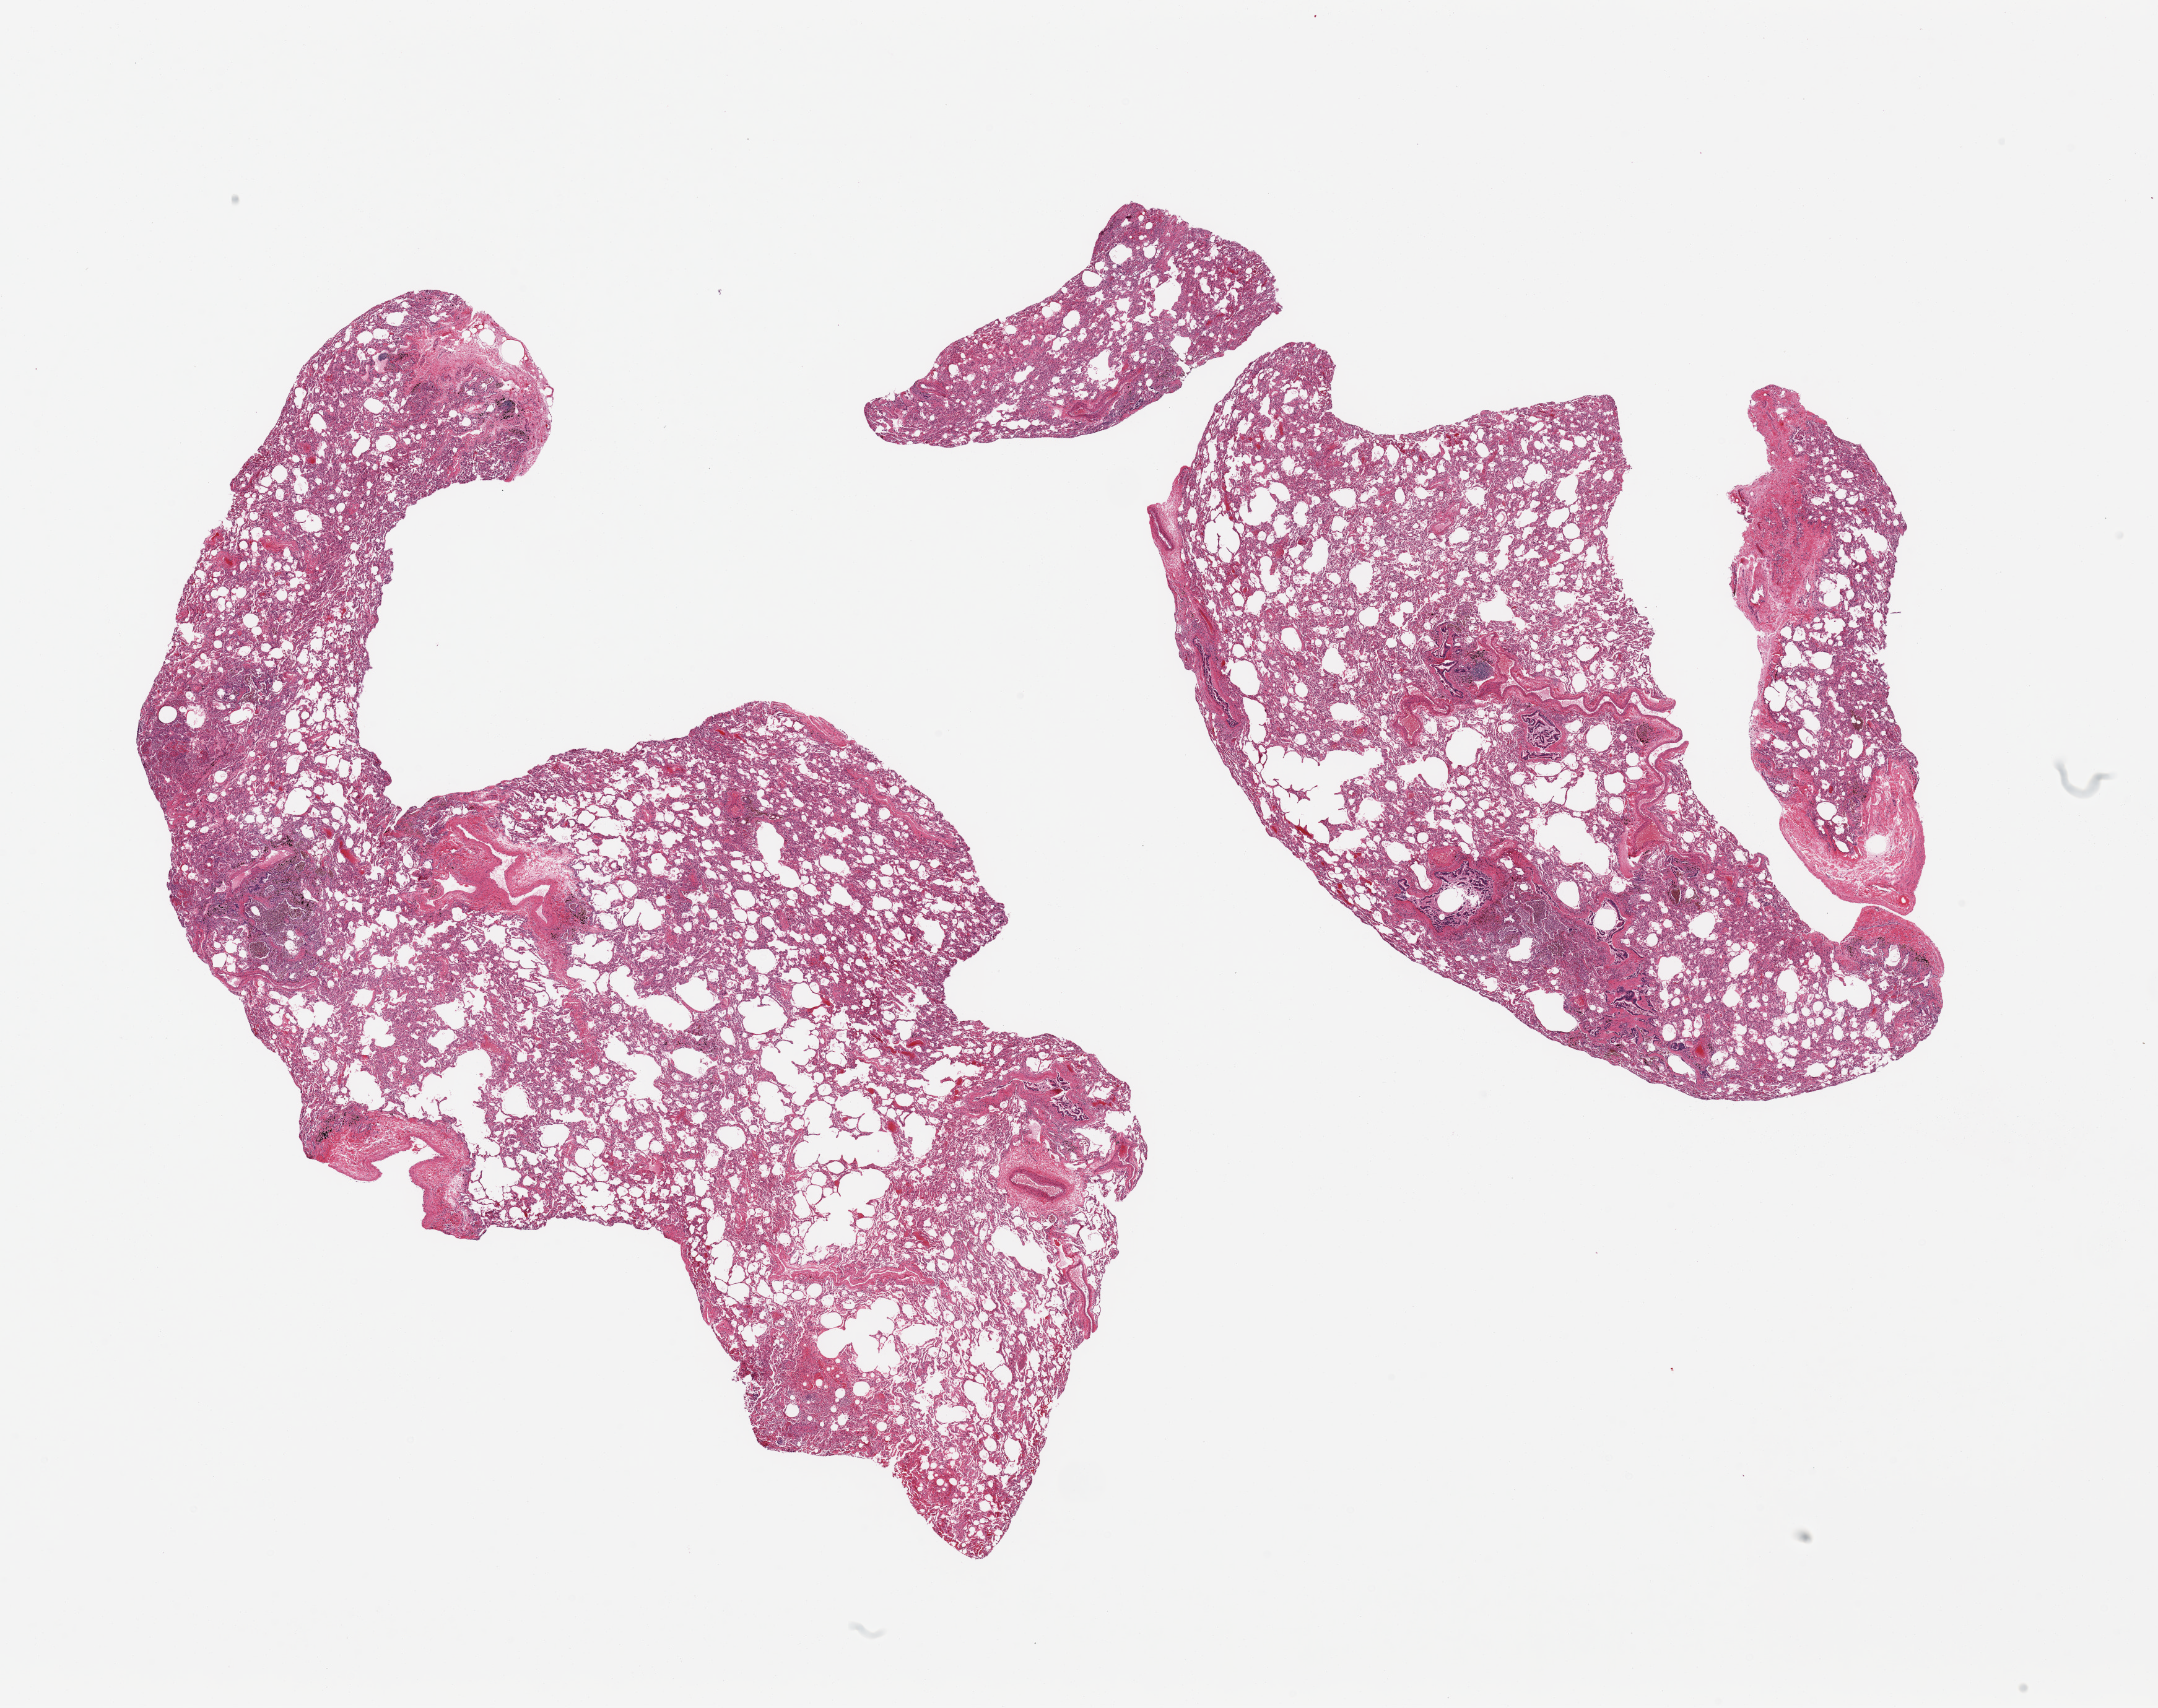
Hematoxylin and eosin (H&E) whole-slide image, shown as a low-resolution overview of the whole scanned area (about 27.6 x 21.8 mm, slide scanned at 20x), PAXgene-fixed, paraffin-embedded tissue, section of lung (target tissue), tissue donor sample. Donor: male.
Pathologist's review note for this sample: 2 pieces, patchy acute pneumonia; Evidence of chronic congestion.